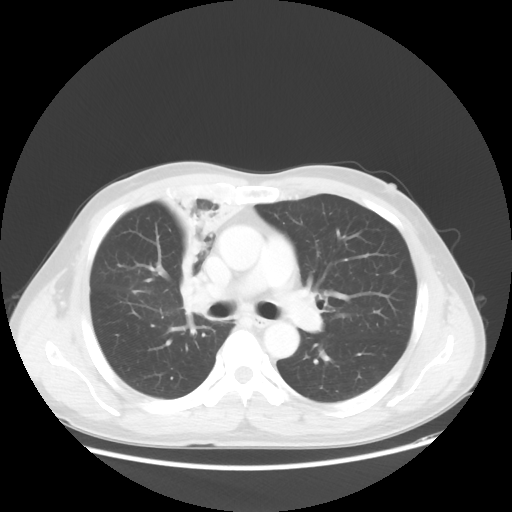
Chest CT, one axial slice. Reconstruction kernel STANDARD. 100 kVp. Lung window (W 1500 / L -600 HU). 5 mm slice thickness. 512 × 512 image matrix. Patient: male, 60 years. Case-level facts recorded for this patient, not image findings: clinical TNM (as recorded): T2a N1 M0.
Structures marked on this image (bounding box drawn by a radiologist):
- lung tumour (recorded histology: squamous cell carcinoma): box from (x=155, y=181) to (x=256, y=271) px